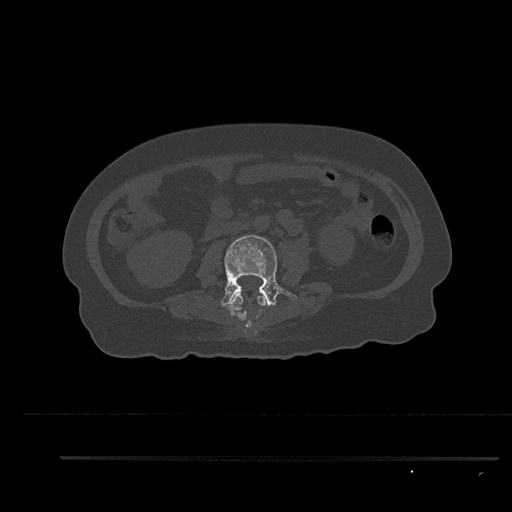
CT including the spine, one axial slice. Reconstruction kernel Br40s/3. 120 kVp. Bone window (W 1800 / L 400 HU). 512 × 512 image matrix. Patient: female, 44 years. From the clinical record (not read from this slice): primary cancer: renal; vertebrae with lytic lesions (as recorded): L1.
Annotated regions visible in this slice (semi-automatically segmented with operator editing):
- L2 vertebra: bounding box (x1, y1, x2, y2) in pixels: (230, 293, 266, 328)
- L3 vertebra: (221, 235, 297, 312)